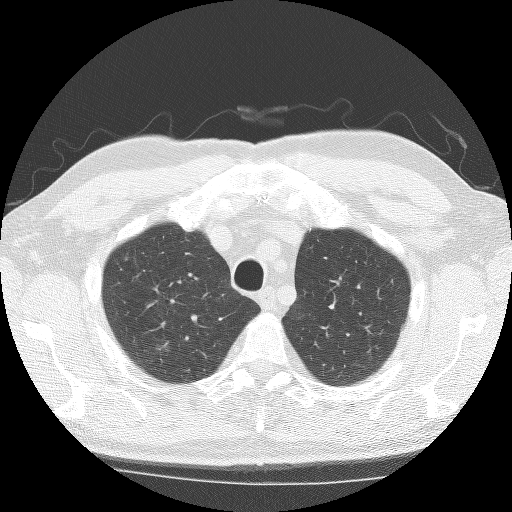
Low-dose screening chest CT, axial slice; baseline annual screen; lung window (W 1500 / L -600 HU); lung (sharp) reconstruction kernel (BONE); 512 × 512 image matrix. Male participant, aged 74 years at enrolment. Former smoker at enrolment.
- Lesion marked by an expert reader, bounding box <140,329,193,372> (left, top, right, bottom; pixels).
- The screening reader recorded 3 non-calcified nodules or masses ≥4 mm on this exam; which of them this box marks is not recorded.
- Official screen result: positive, change unspecified: nodule(s) >= 4 mm or enlarging nodule(s), mass(es), or other non-specific abnormalities suspicious for lung cancer.
- Later outcome: lung cancer diagnosed 140 days after this screen — bronchiolo-alveolar carcinoma, non-mucinous, right upper lobe, stage IA (AJCC 6th edition), 14 mm at pathology.